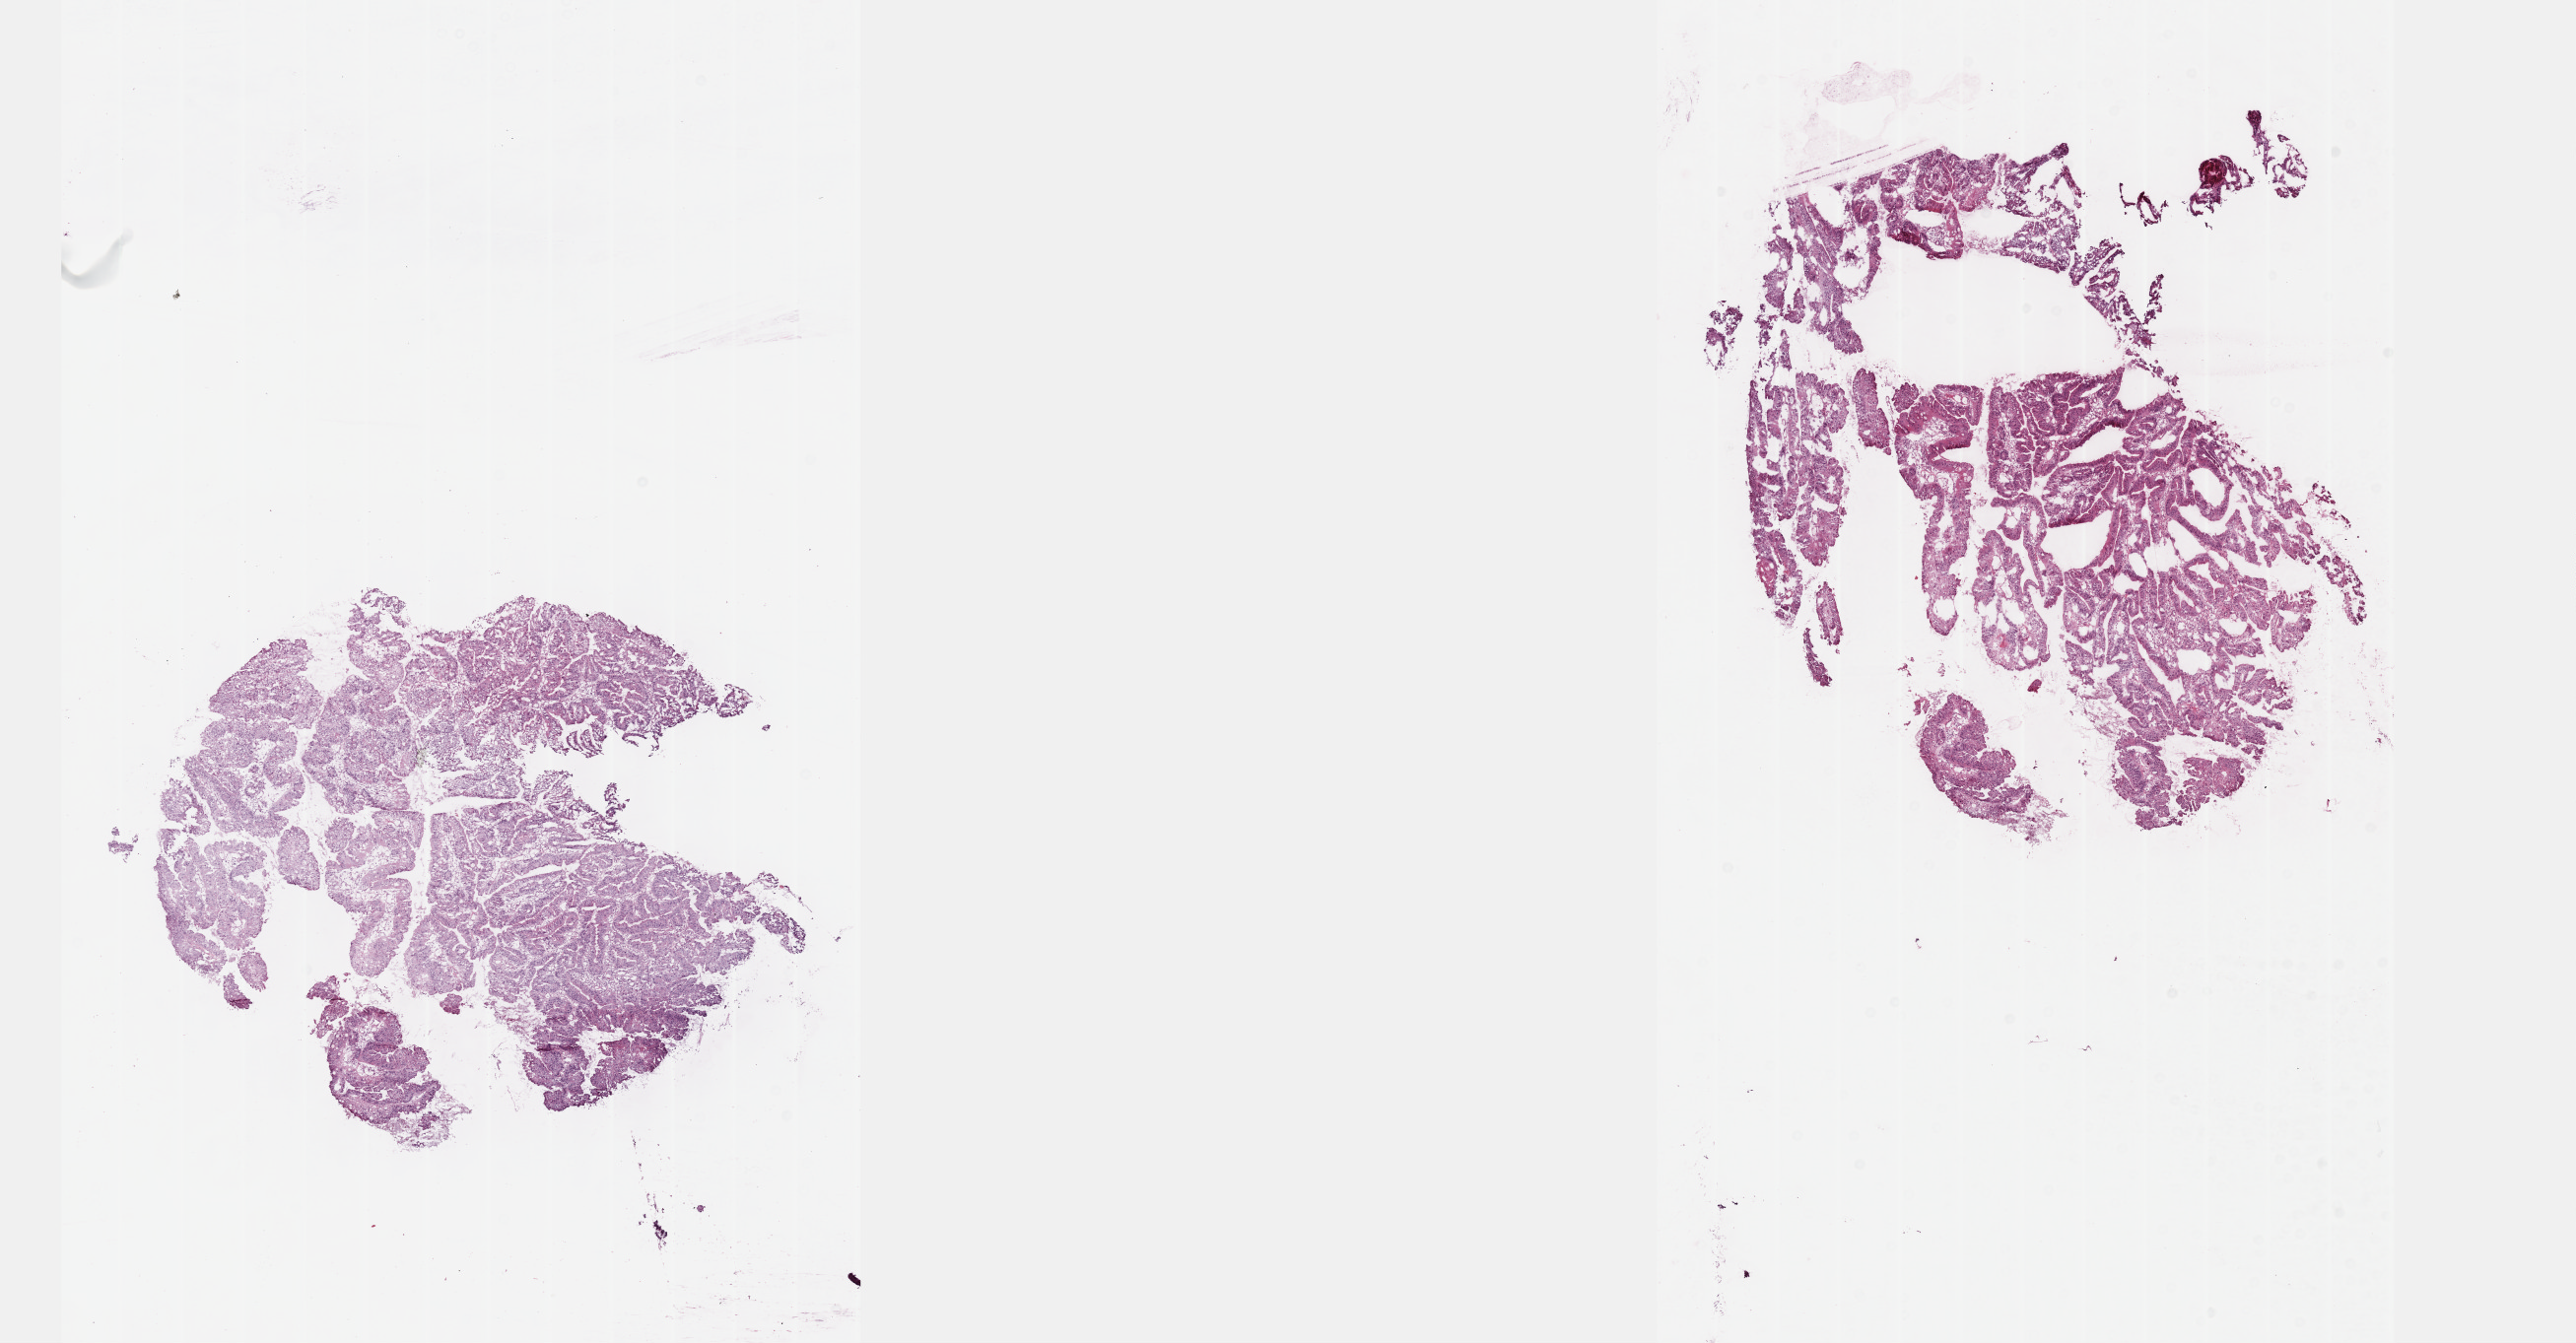
Whole-slide histology image, H&E — a low-resolution overview of the entire scanned area, about 21.1 x 11.0 mm; frozen section; sample: primary tumour, colon. Male, age 67 years at initial diagnosis. Pathologist review of this section (percent, as recorded): tumour cells 85%, tumour nuclei 90%, normal cells 0%, stromal cells 14%, necrosis 1%. Inflammatory infiltration, as recorded: lymphocyte infiltration 4%, monocyte infiltration 1%, neutrophil infiltration 1%.
Lymph nodes positive (case pathology): 0 of 27 examined. AJCC pathologic stage: II (5th edition). Histologic diagnosis: Adenocarcinoma, NOS (cecum).